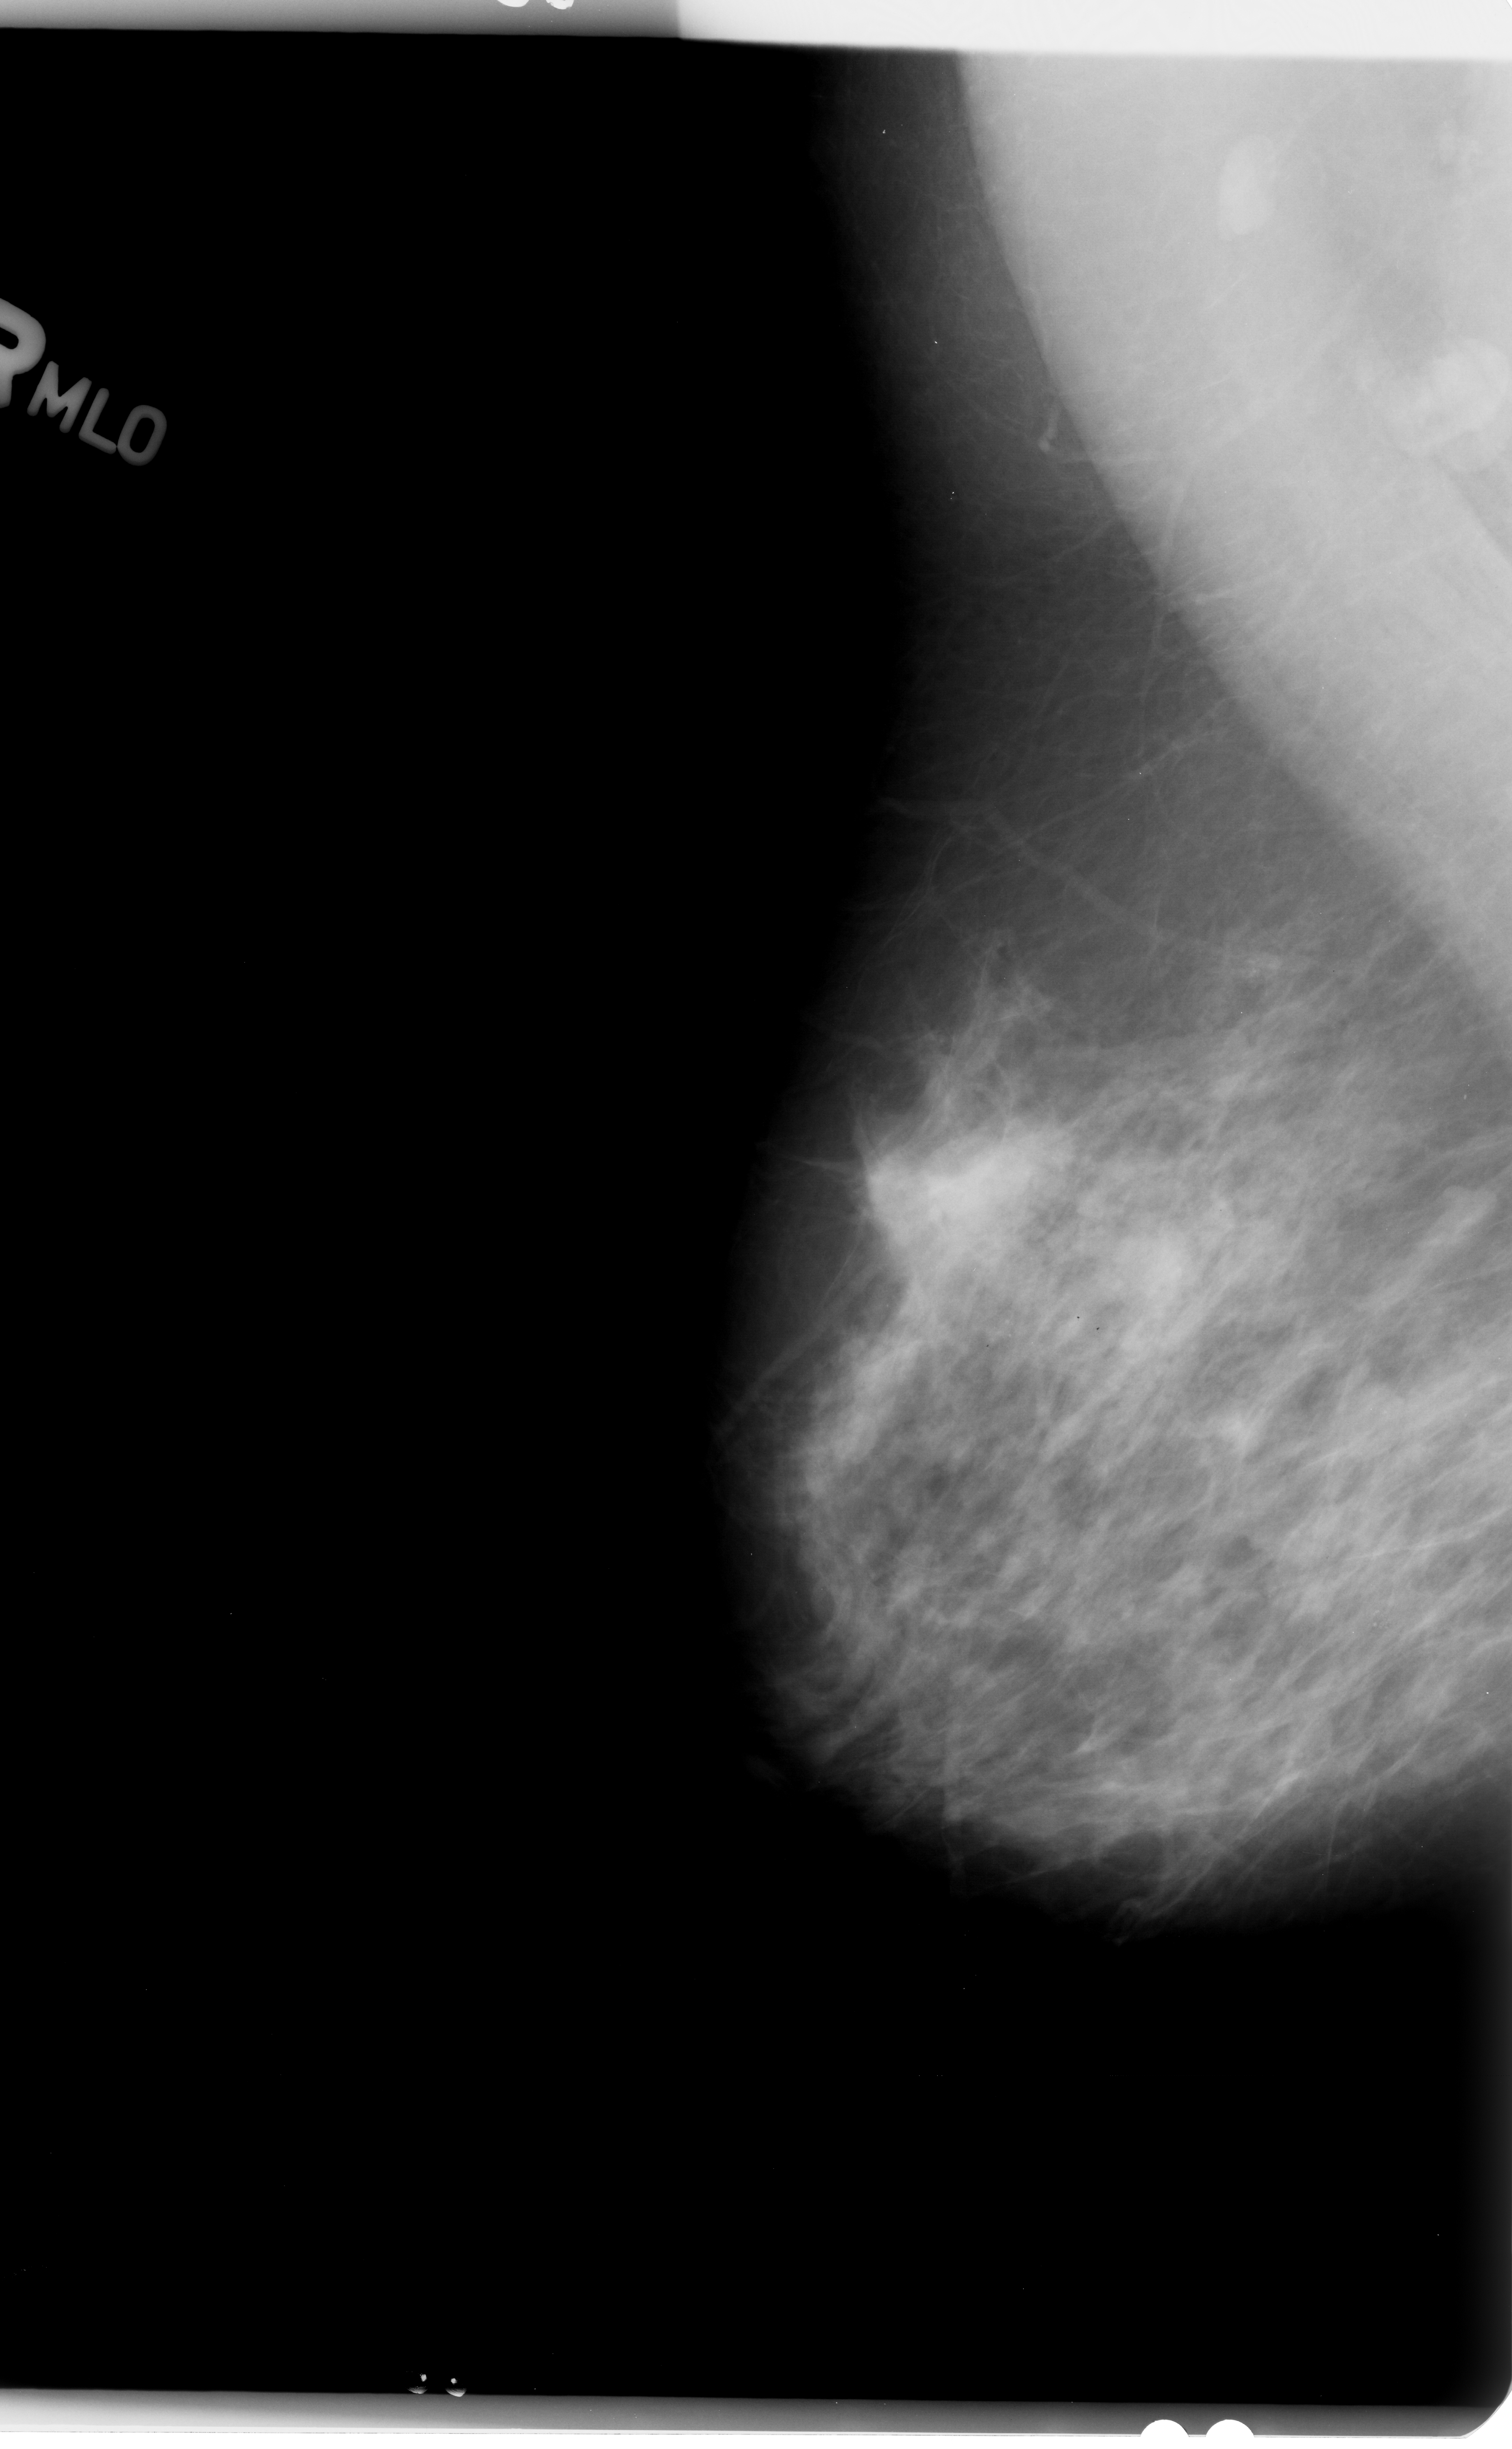
Digitized screen-film mammogram, right breast, MLO view, breast composition: heterogeneously dense (BI-RADS density category 3 of 4).
- Radiologist-marked abnormalities on this image: Finding 1 of 2: calcifications, morphology amorphous / pleomorphic, distribution clustered; BI-RADS assessment category 4; pathology result (as recorded, not read from the image): benign.
- Finding 2 of 2: calcifications, morphology amorphous / pleomorphic, distribution clustered; BI-RADS assessment category 4; pathology result (as recorded, not read from the image): benign.